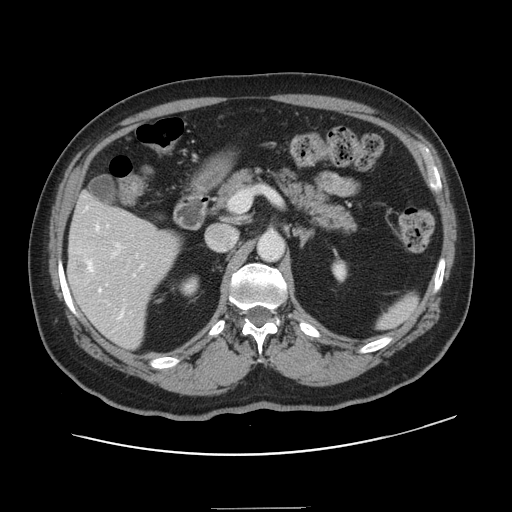
Contrast-enhanced abdominal CT, one axial slice; slice 75 of 143 in the series (ordered by position); 120 kVp; intravenous contrast given; soft-tissue window (W 400 / L 40 HU); 2.5 mm slice thickness; 512 × 512 image matrix, field of view 402 × 402 mm. Male patient, age 62 years. Case-level facts recorded for this patient, not image findings: diagnosis: colorectal cancer liver metastases, imaged before liver resection; multiple liver metastases: yes; largest metastasis: 2.7 cm; chemotherapy before resection: yes.
Outlined on this slice (outlined manually by an expert reader):
- hepatic veins: bounding box [x1, y1, x2, y2] px = [86, 206, 143, 319]
- liver: [68, 196, 179, 348]
- planned liver remnant (the part of the liver to remain after resection): [74, 196, 133, 225]
- portal vein (with intrahepatic branches): [113, 243, 122, 256]
- liver metastasis: [80, 265, 84, 269]